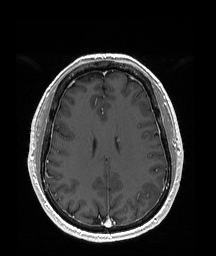
Brain MRI from a brain-tumour surgery series, one axial slice. T1-weighted post-contrast. 1 mm slice thickness. 216 × 256 image matrix, field of view 219 × 260 mm. Case-level facts recorded for this patient, not image findings: histopathology: Glioblastoma; WHO grade: 4; IDH mutation: no; tumour location: Left Temporal Parietal.
Outlined on this slice (manually delineated by an expert):
- tumour: bounding box (x1, y1, x2, y2) in pixels: (143, 182, 163, 208)